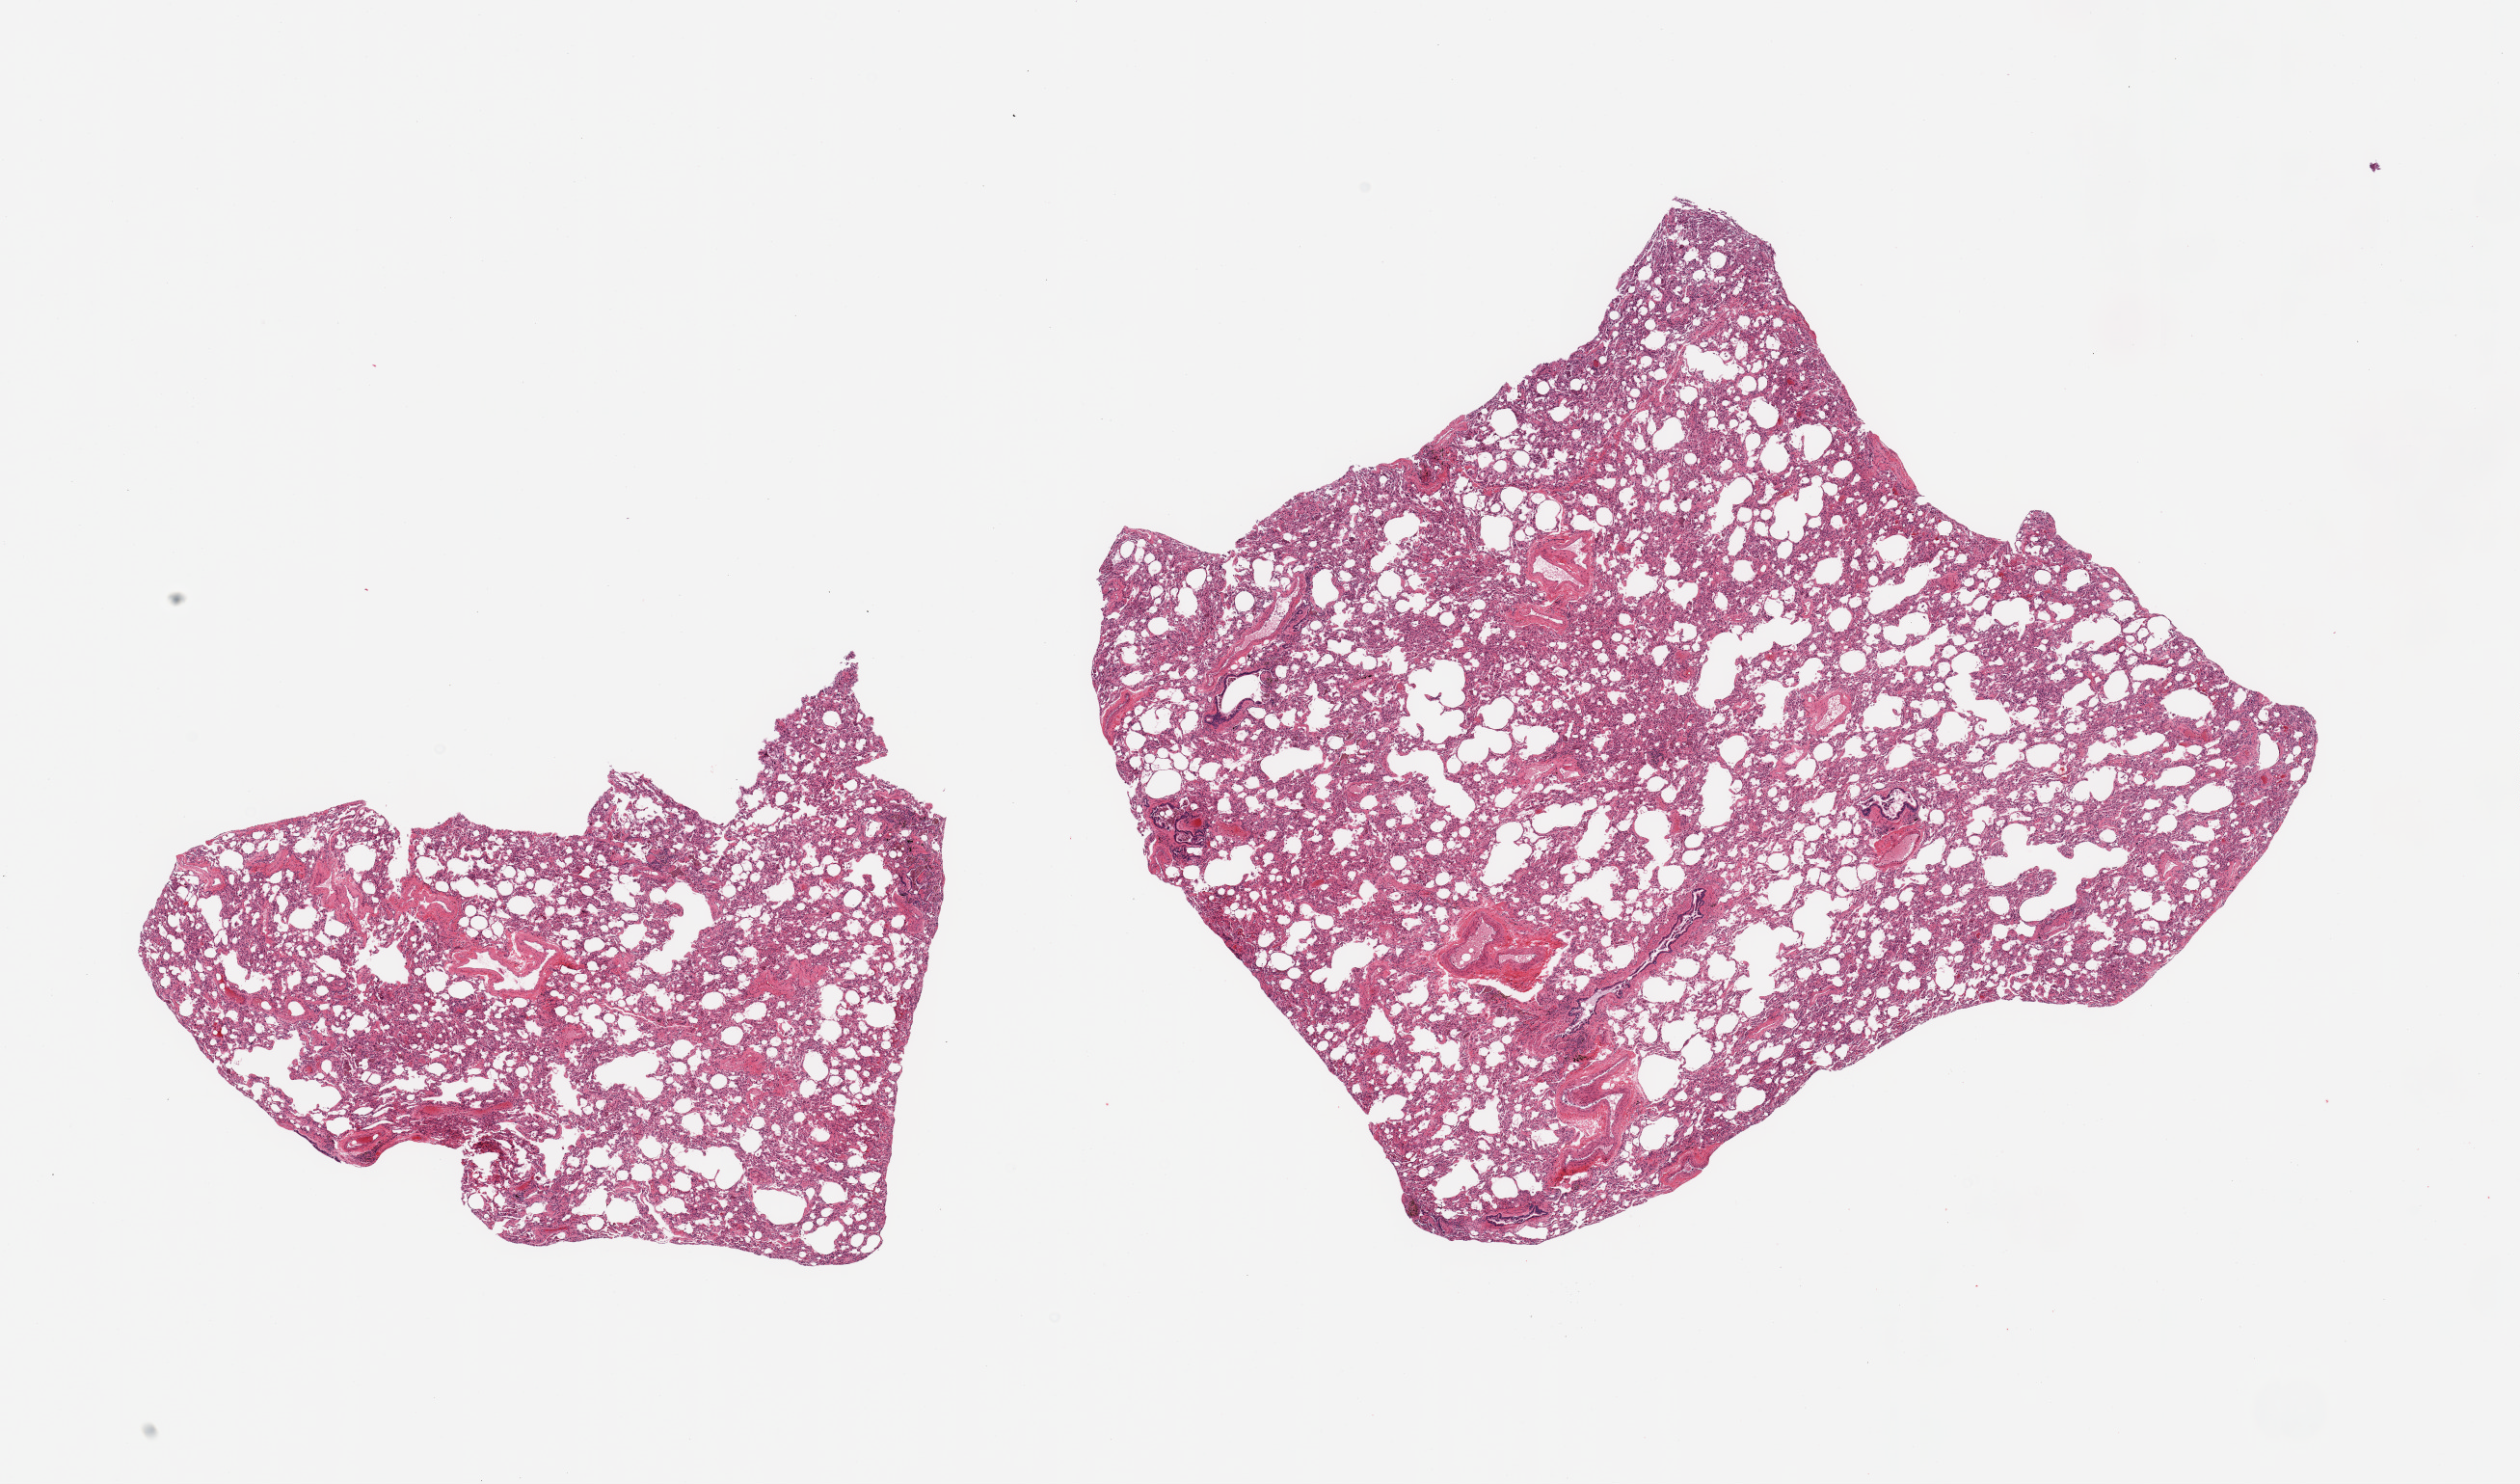
Whole-slide image, haematoxylin and eosin stain — whole scanned area (about 20.7 x 12.2 mm) shown as a low-resolution overview, PAXgene-fixed paraffin-embedded (PFPE) section, section of lung (target tissue), donor tissue sample.
Reviewer comment on this tissue sample: 2 pieces; some bronchi have pigmented macrophages.